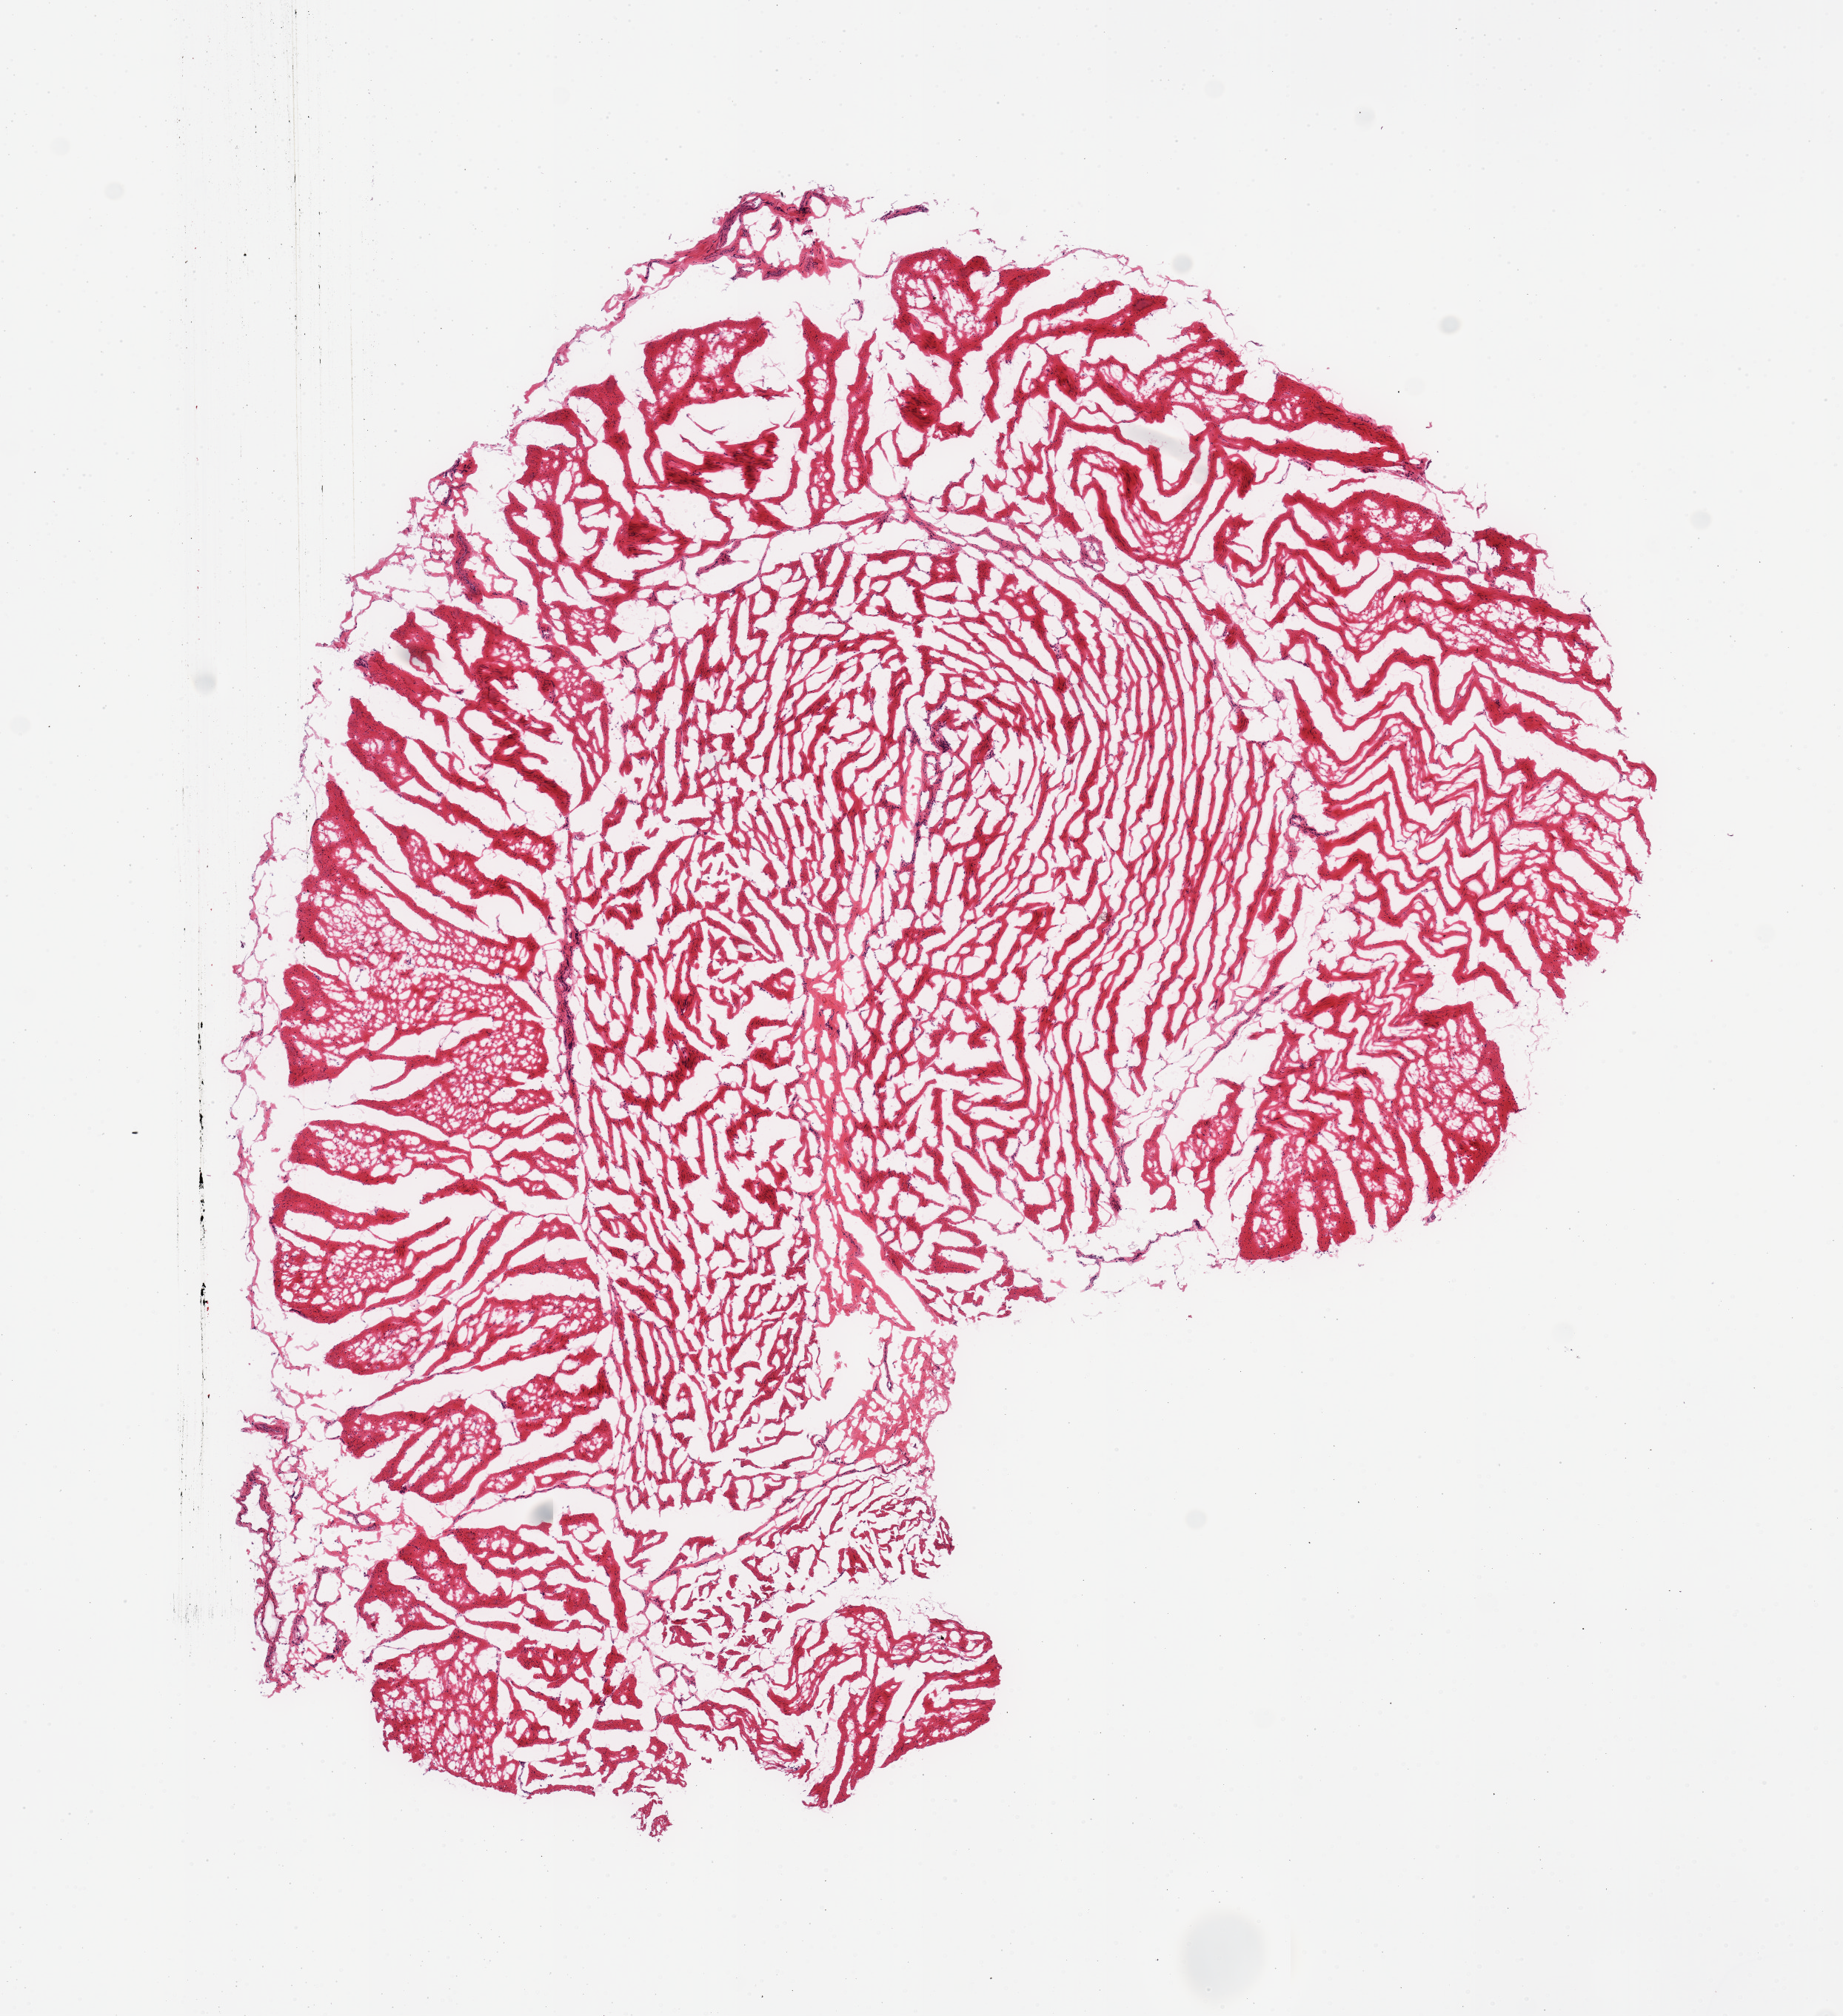
Whole-slide image, H&E stain, shown as a low-resolution overview of the whole scanned area (about 9.8 x 10.8 mm, acquisition: 20x scan); frozen section (dry ice); section of esophageal muscle (target tissue); tissue donor sample. Female donor.
- review note (as recorded): 1 piece; skeletal muscle with minimal fat content; no sign of crystalline contaminants